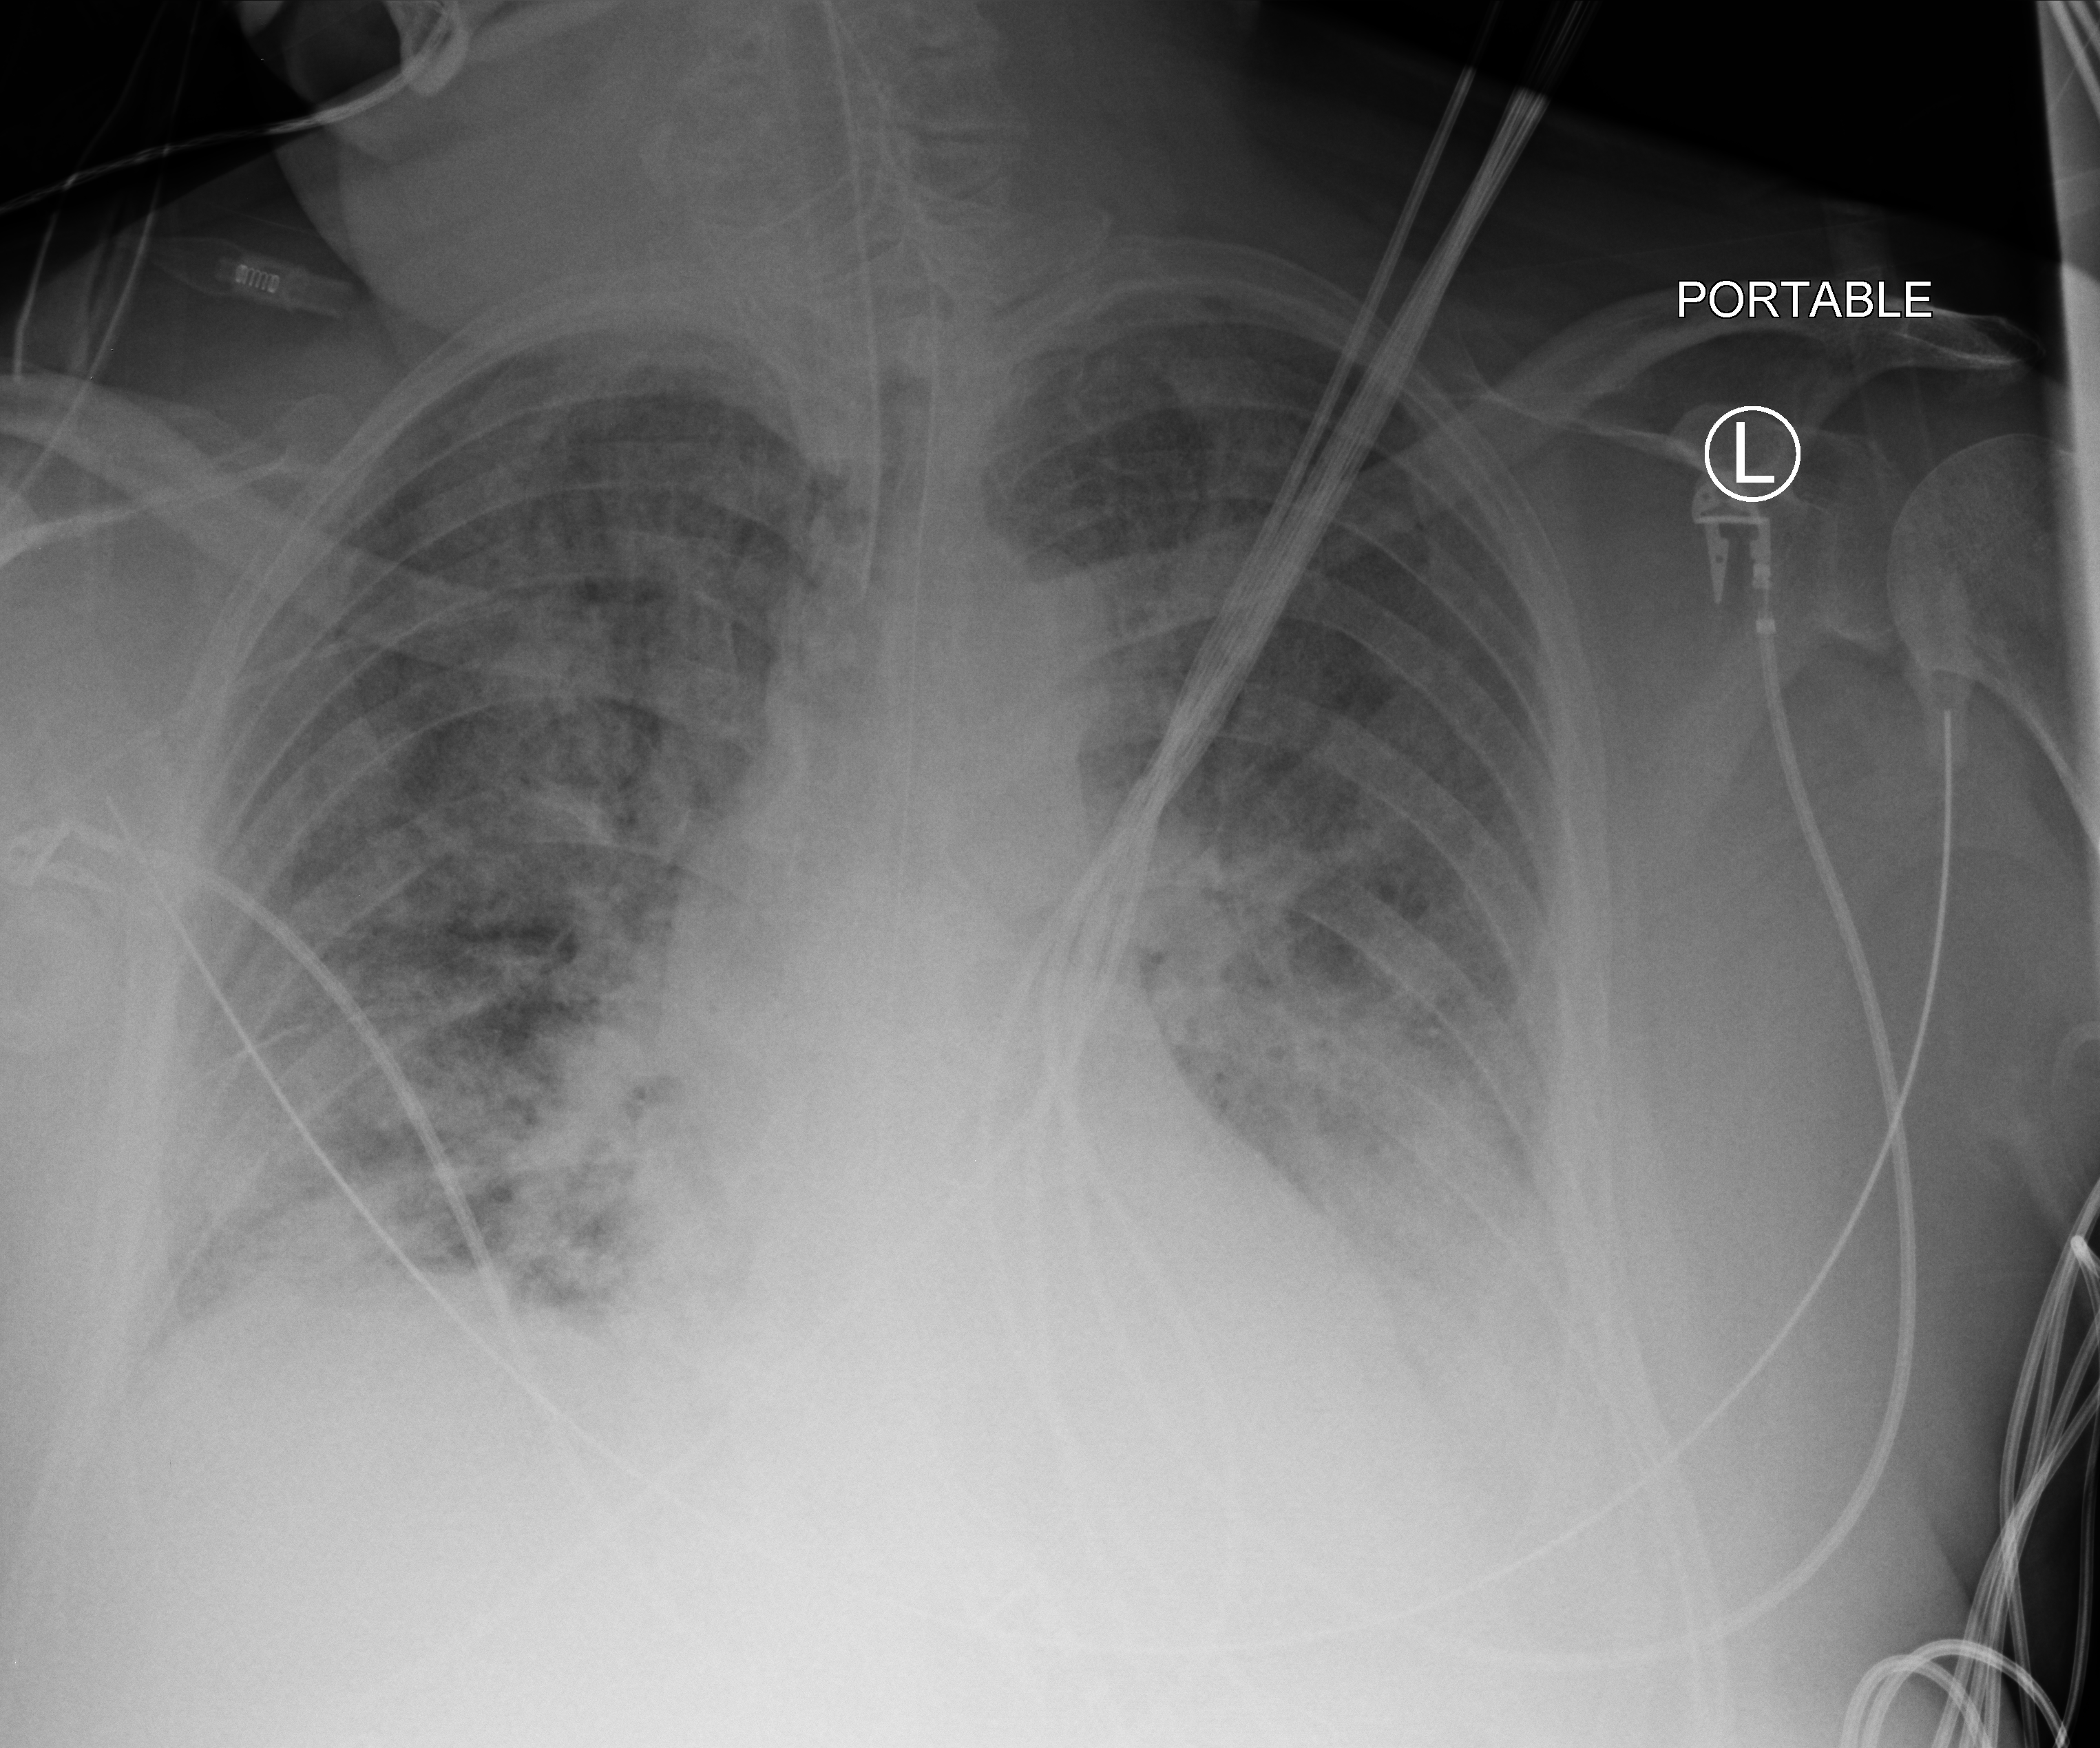
Portable chest radiograph; anteroposterior (AP) projection. Patient hospitalised with COVID-19; male, aged 60–74 years.
Admission-level facts for this patient (not findings on this image; timing relative to this image not recorded): admitted to intensive care during this hospital stay: yes; mechanically ventilated during this hospital stay: yes; diabetes (admission record): no.